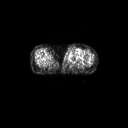
FDG PET of an extremity soft-tissue mass (from a PET/CT study), one axial slice; slice 47 of 91 in the series (ordered by position); 3.27 mm slice thickness; 128 × 128 image matrix, field of view 700 × 700 mm. Female patient, age 74 years. Case-level facts recorded for this patient, not image findings: histological type: pleomorphic leiomyosarcoma; grade: high; site of the primary tumour: left thigh.
Outlined on this slice (expert contour drawn on MRI and transferred to this co-registered scan by the dataset authors):
- gross tumour volume including surrounding oedema: box from (x=65, y=48) to (x=78, y=61) px